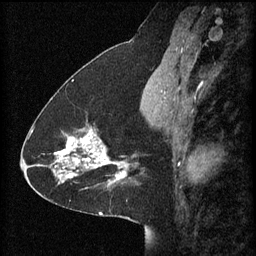
Breast MRI (dynamic contrast-enhanced), one sagittal slice; slice 29 of 60 in the series (ordered by position); 3 images stored at this slice position (order not interpretable as contrast timing); 1.5 T; TE 4.2 ms, TR 8.2 ms; 2 mm slice thickness; 256 × 256 image matrix, field of view 200 × 200 mm. Female patient, age 41 years.
Outlined on this slice (semi-automatic segmentation, software-assisted and operator-edited):
- analysis volume of interest (the breast-tissue region the enhancement analysis was run in; not a lesion): bounding box <58,120,128,181> (left, top, right, bottom; pixels)
- tumour enhancement mask (voxels above the 70 % enhancement threshold inside the analysis volume of interest): <58,130,128,181>